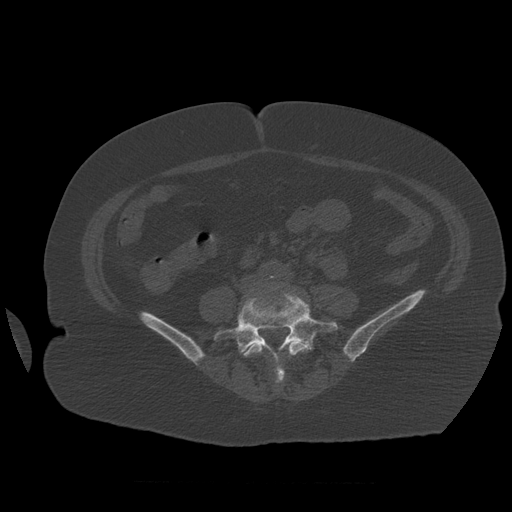
CT including the spine, one axial slice; slice 191 of 399 in the series (ordered by position); reconstruction kernel STANDARD; 120 kVp; bone window (W 1800 / L 400 HU); 1.25 mm slice thickness; 512 × 512 image matrix, field of view 404 × 404 mm. Patient age 81 years. From the clinical record (not read from this slice): primary cancer: renal; vertebrae with lytic lesions (as recorded): L1.
Annotated regions visible in this slice (semi-automatically segmented with operator editing):
- L4 vertebra: bounding box <244,338,310,383> (left, top, right, bottom; pixels)
- L5 vertebra: <214,294,338,355>